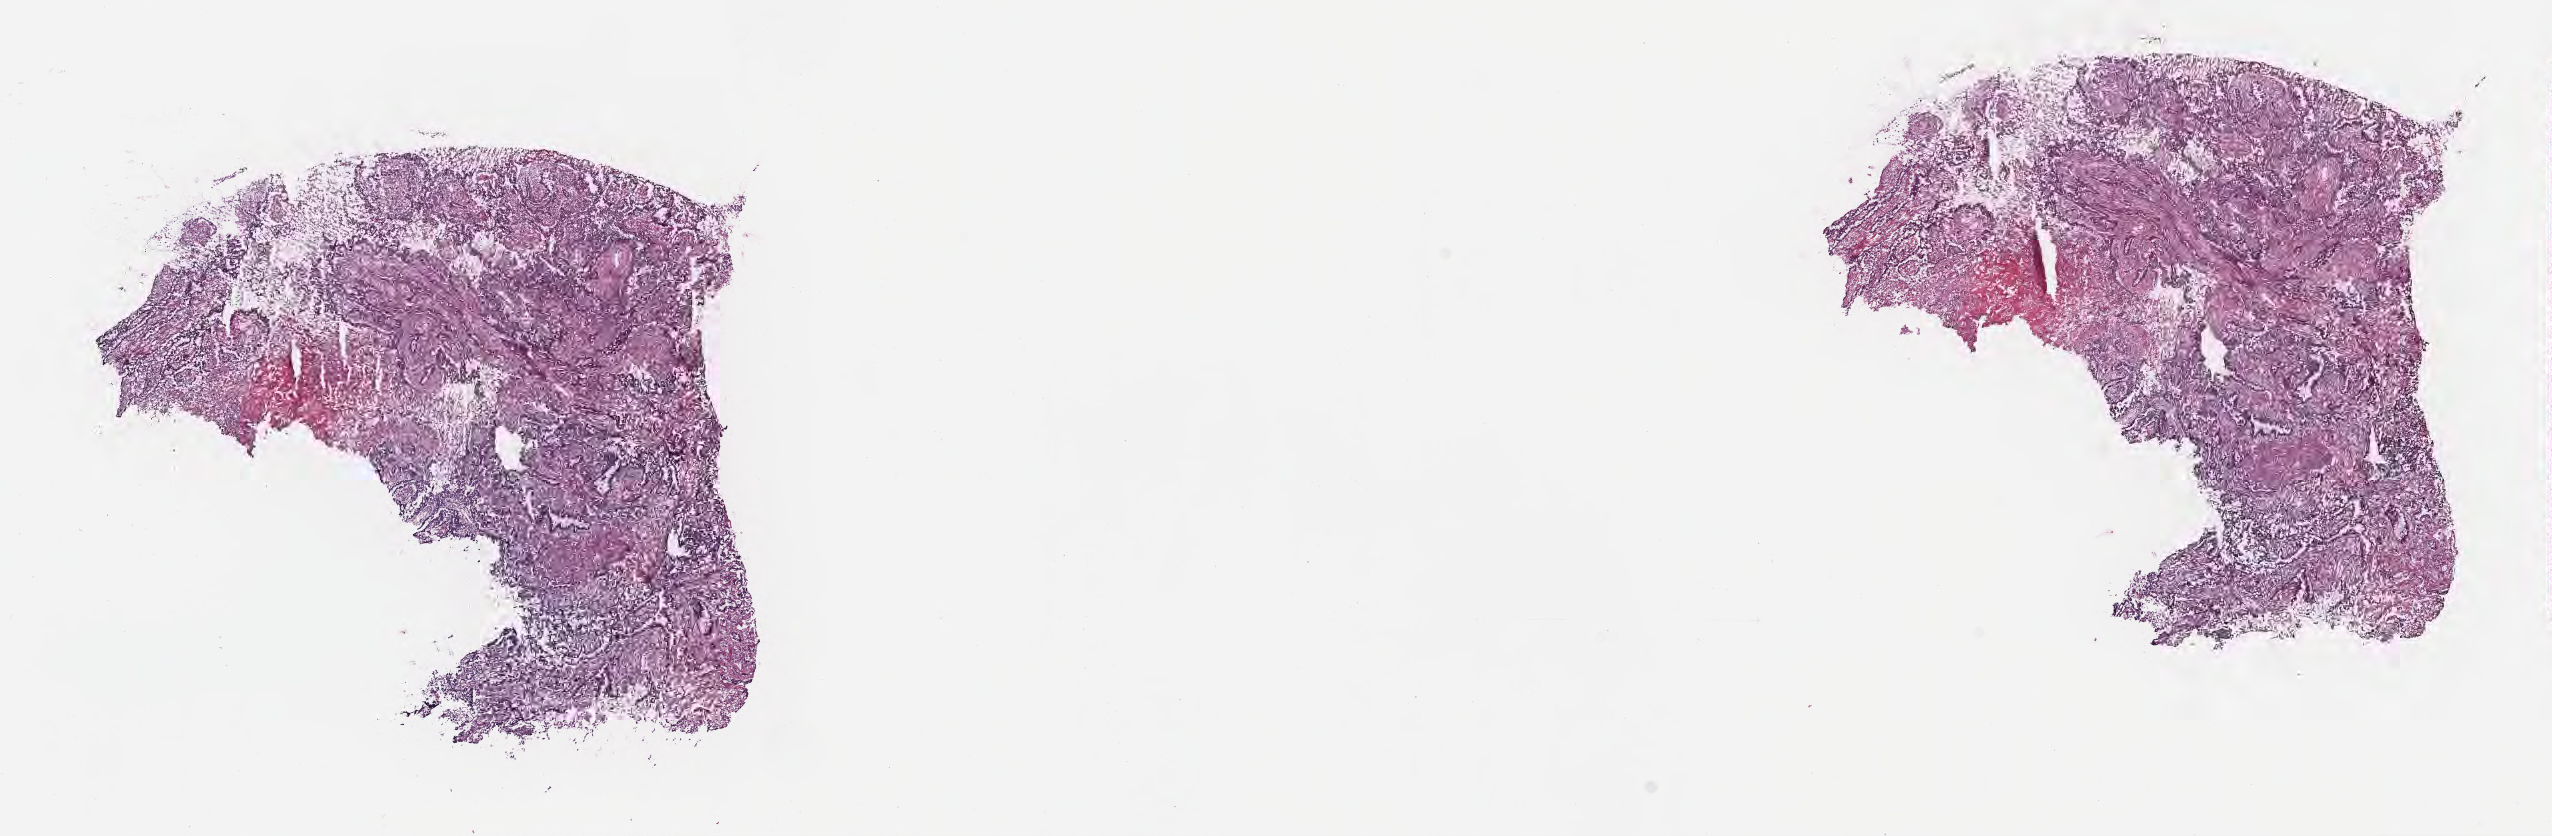
Haematoxylin and eosin whole-slide image, low-resolution overview of the scanned area, about 20.6 x 6.8 mm; cryosection; primary tumor; site: upper lobe of right lung. Patient male; 68 years old. Pathologist review of this section (percent, as recorded): tumor cells 30%, tumor nuclei 80%, stromal cells 50%, necrosis 20%, normal cells 0%. Inflammatory infiltration, as recorded: lymphocyte infiltration 8%, monocyte infiltration 2%, neutrophil infiltration 1%.
Section: top of the tissue portion. Histologic diagnosis: Adenocarcinoma with mixed subtypes. AJCC pathologic stage: Stage IIIB.